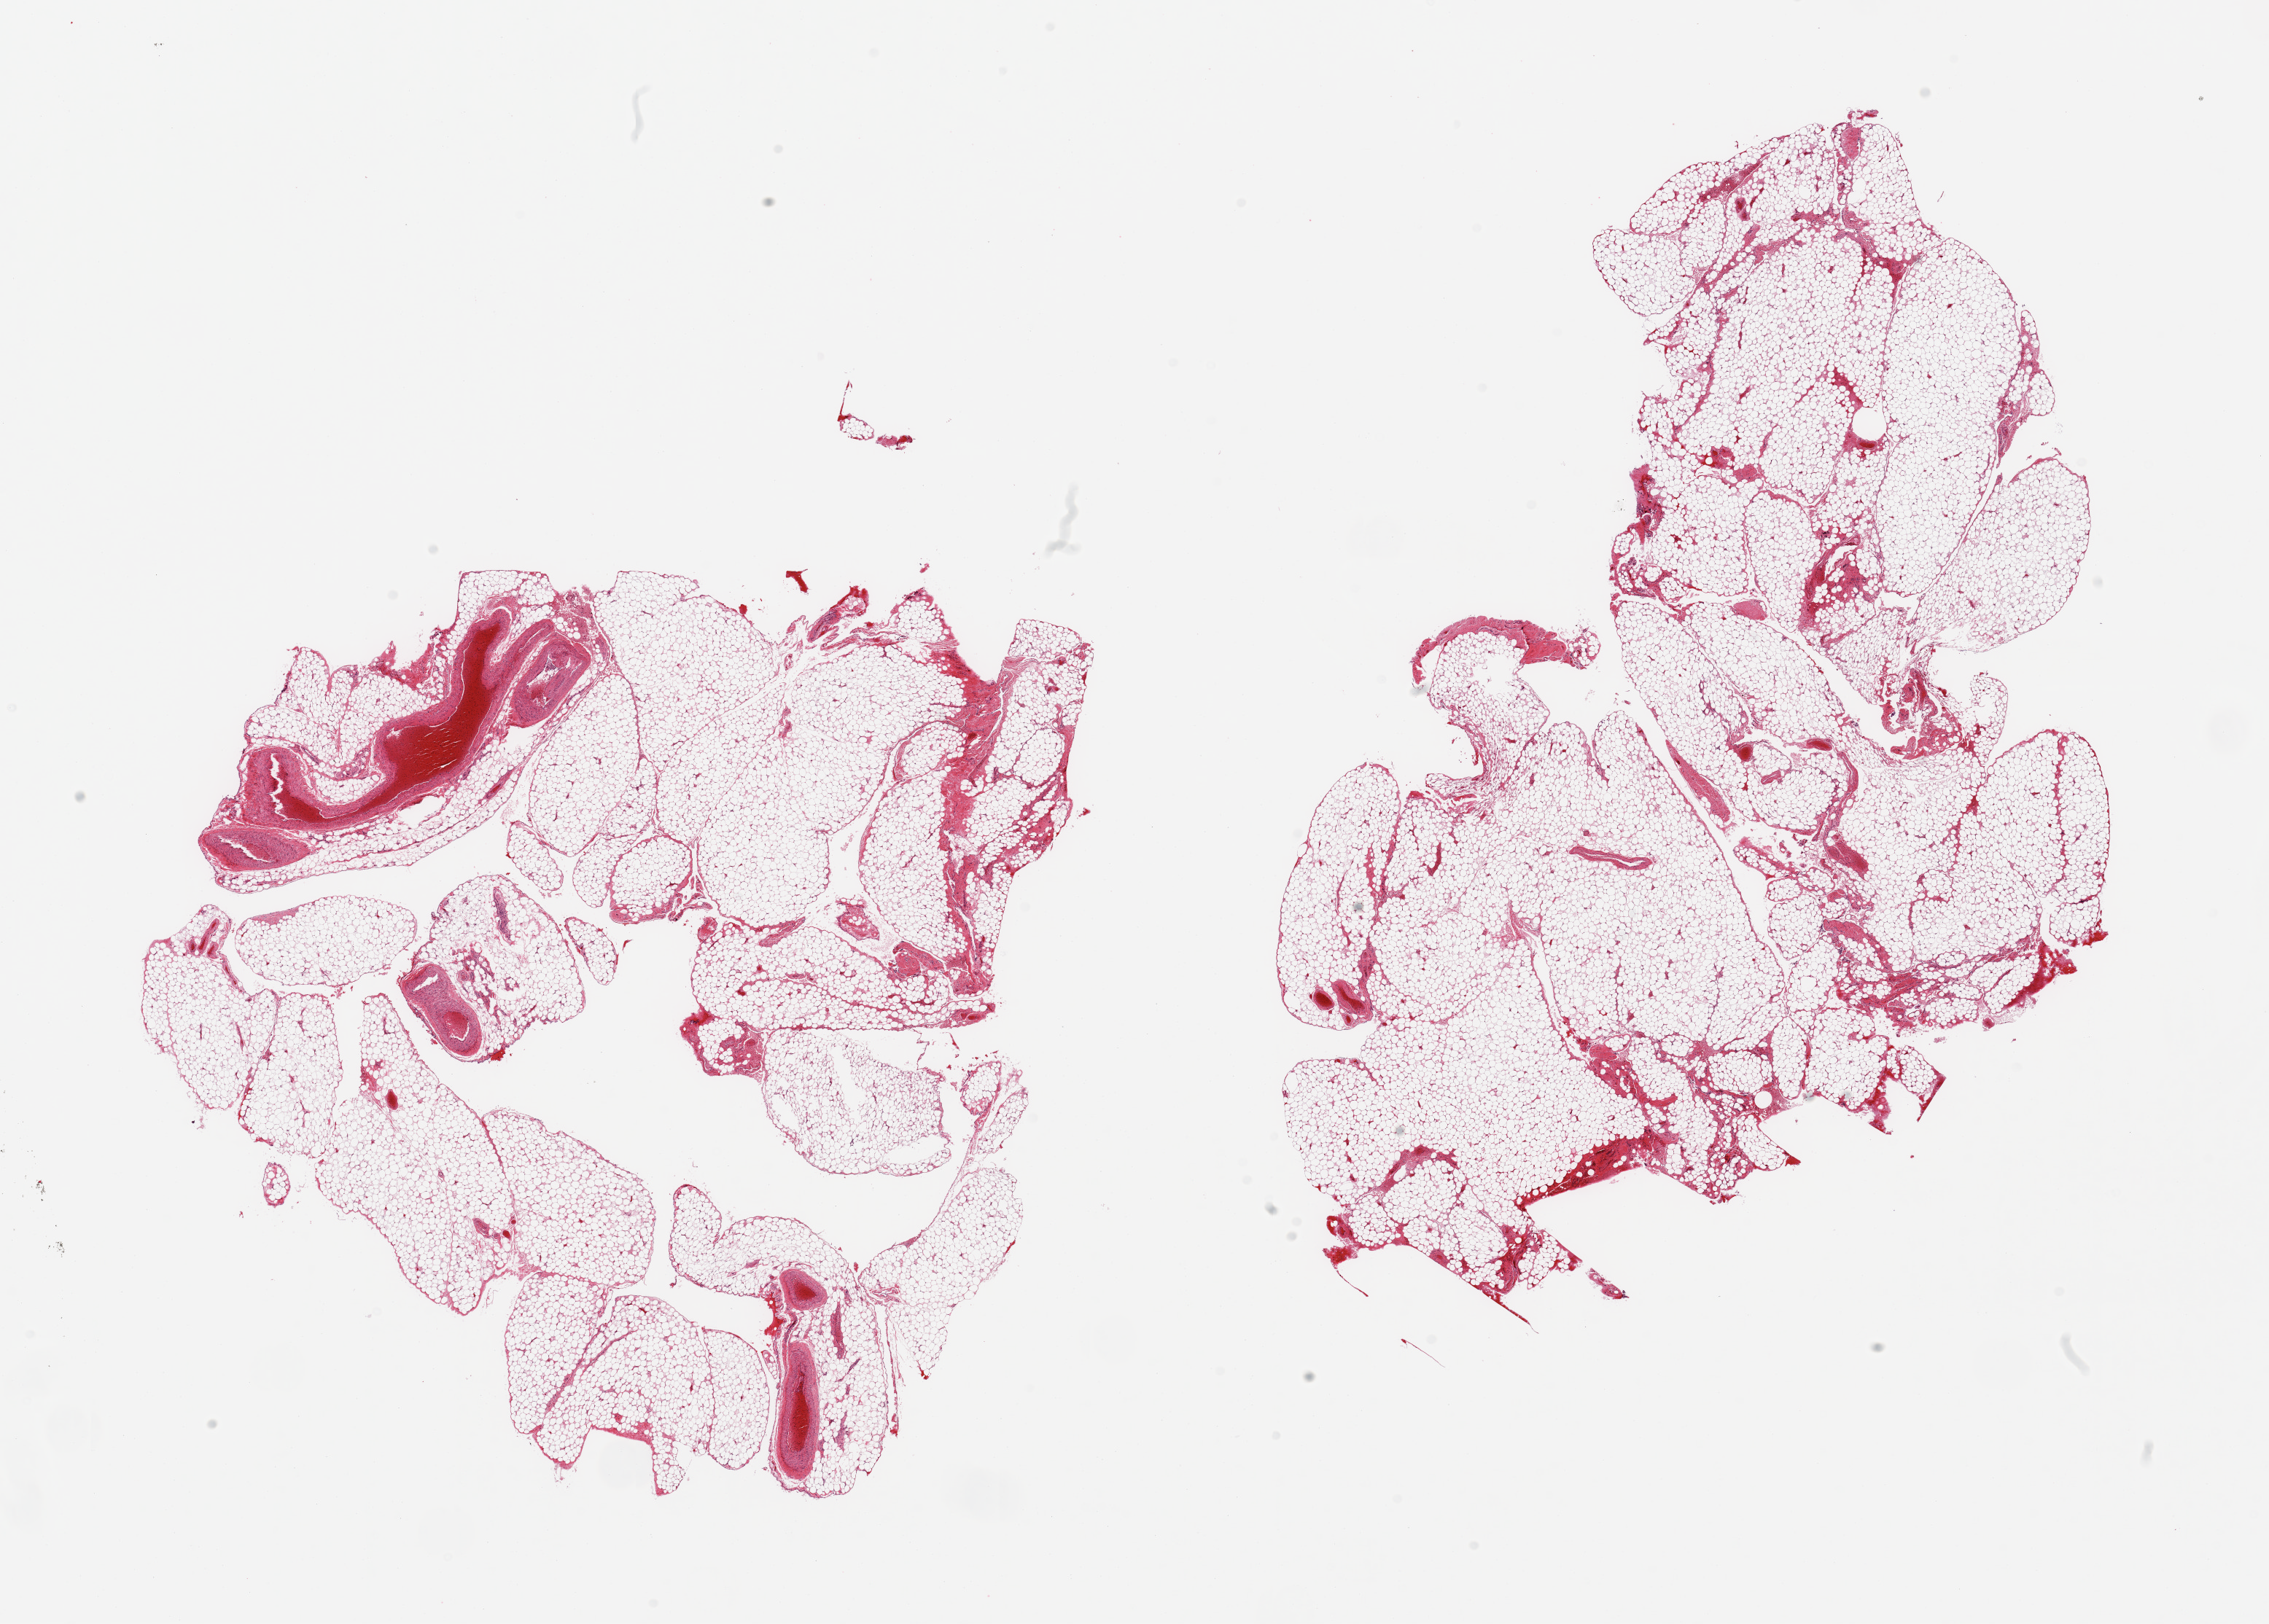
H&E whole-slide image, brightfield, a low-resolution overview of the entire scanned area, about 24.6 x 17.6 mm (slide scanned at 20x); PAXgene-fixed, paraffin-embedded tissue; sampled site (target tissue): omentum; donor tissue sample. Donor sex: male.
Reviewer comment on this tissue sample: 2 pieces, ~10% vascular/fascia elements.